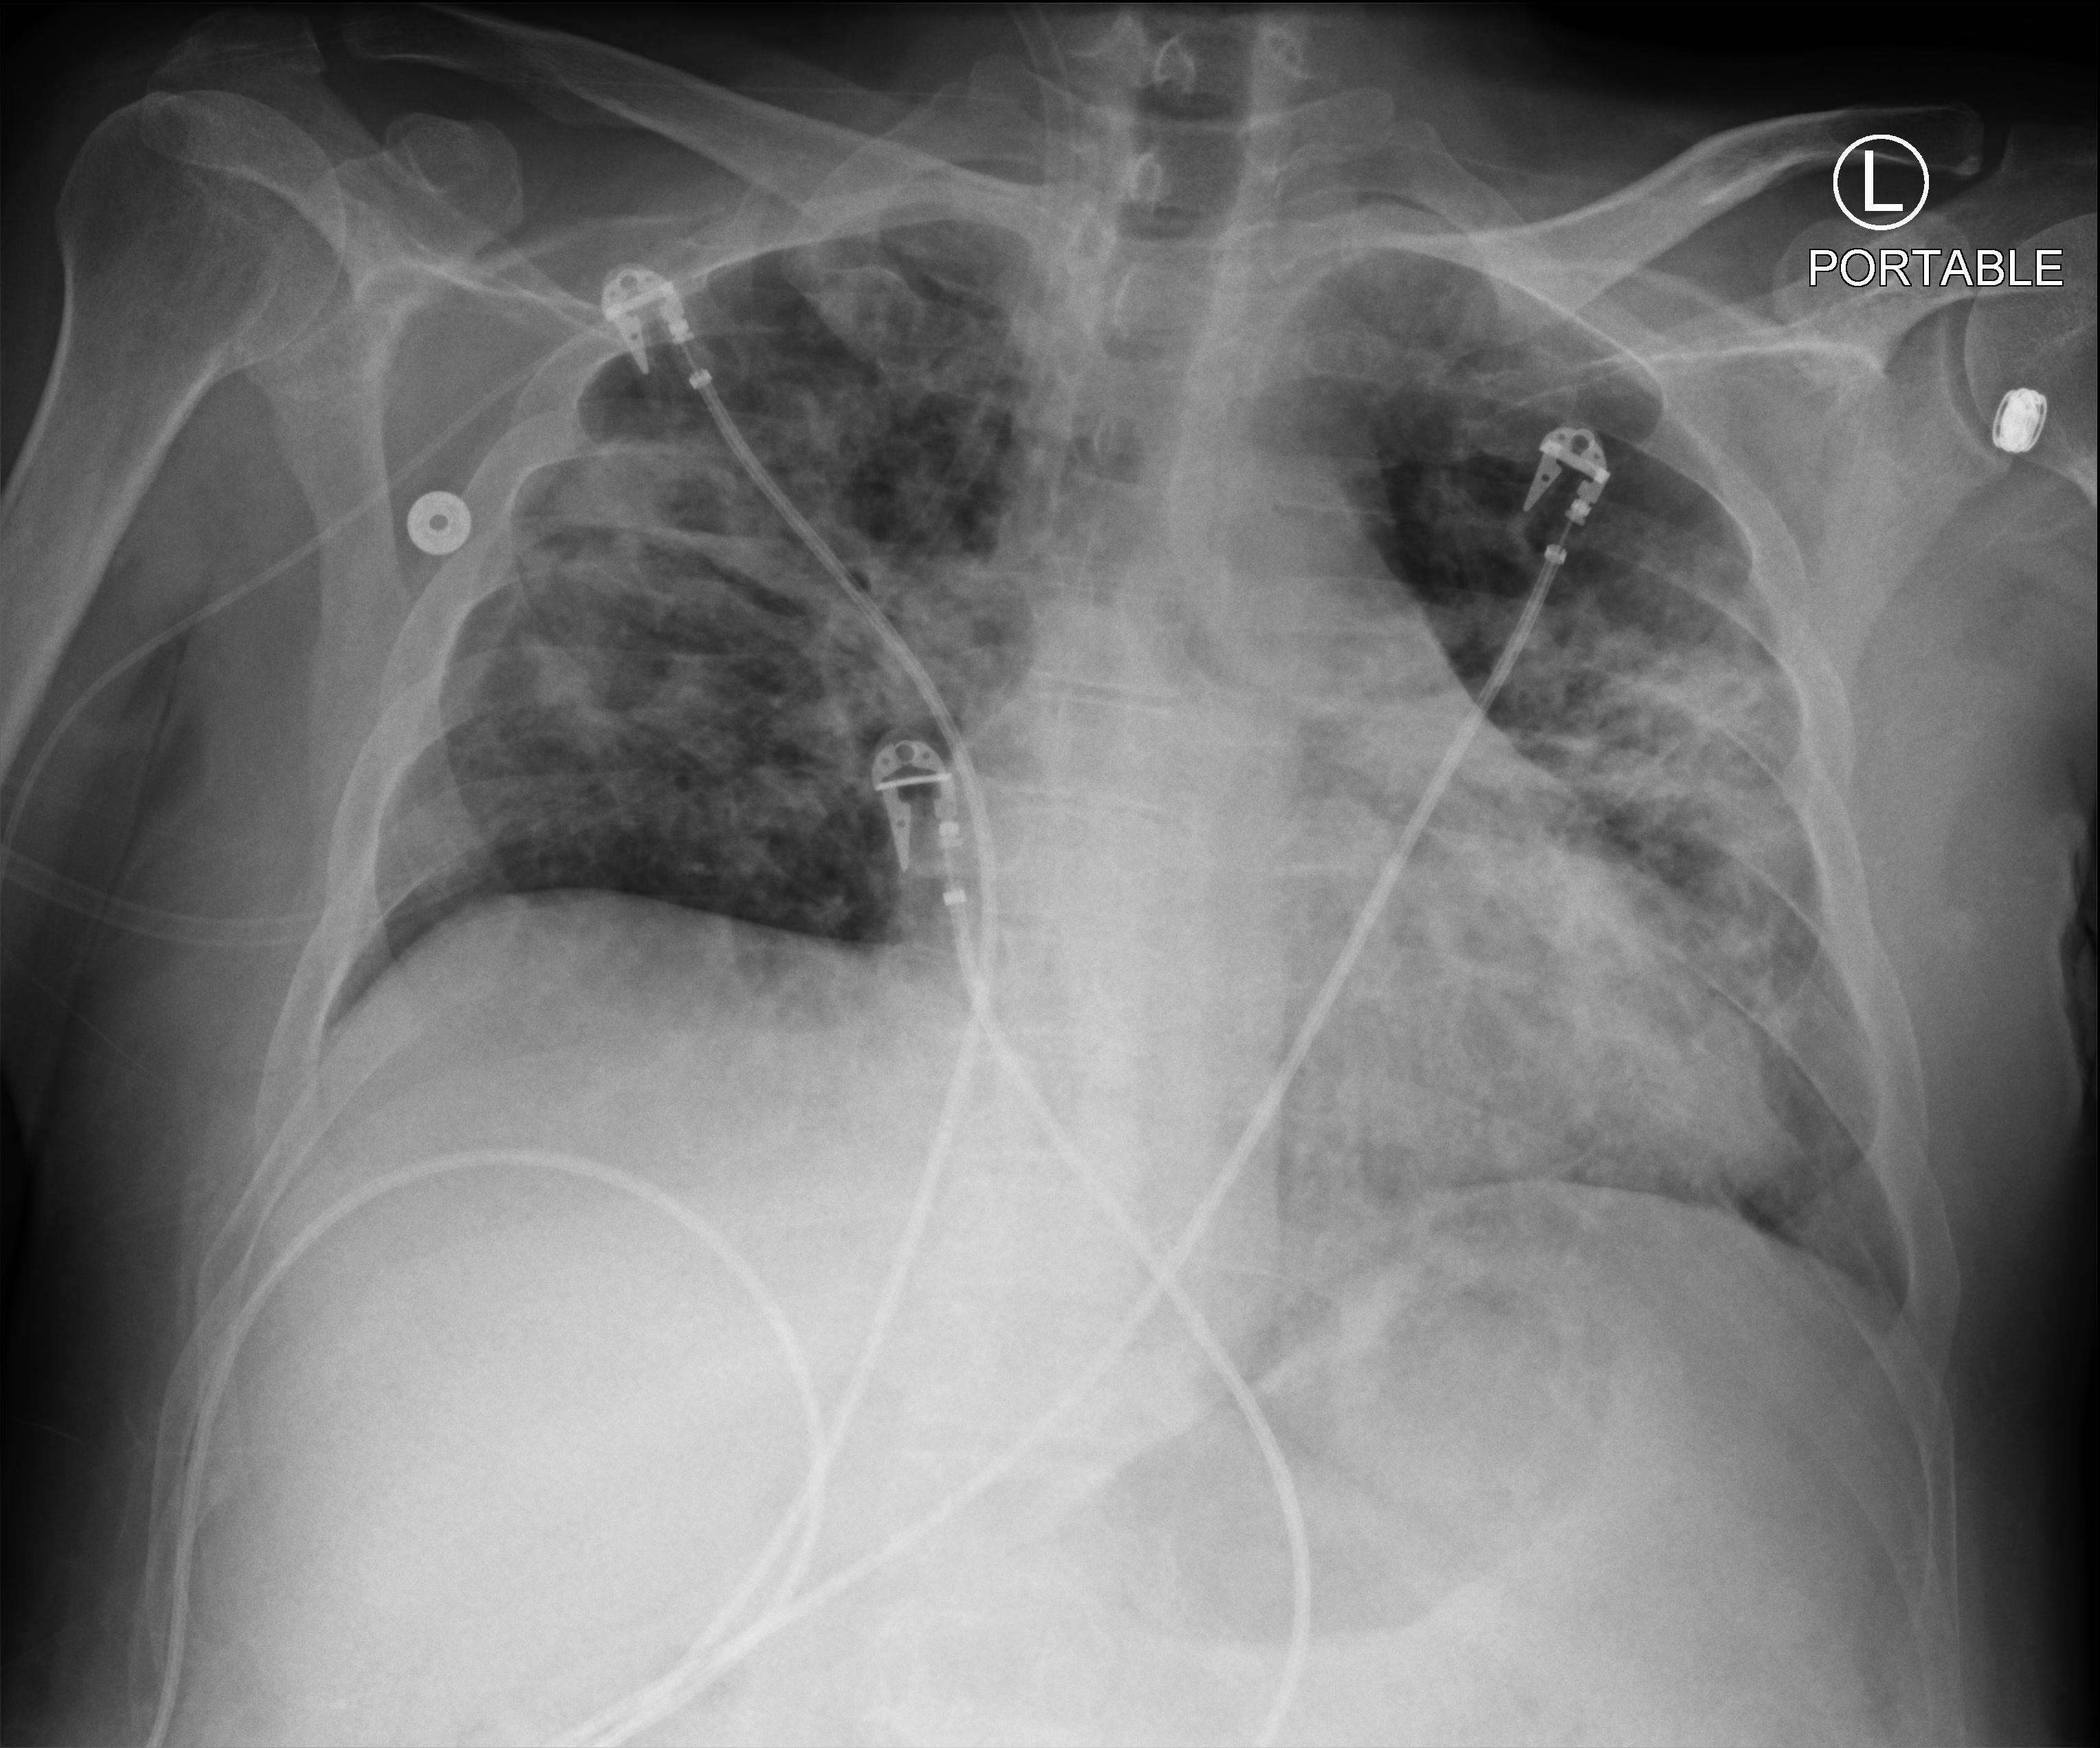
Bedside chest radiograph (computed radiography), anteroposterior (AP) projection. Male patient hospitalised with COVID-19, age 18–59 years.
From the hospital-stay record, not from the radiograph (when in the stay this image was taken is not recorded): other chronic lung disease (admission record): no; length of hospital stay: 20 days; admitted to intensive care during this hospital stay: yes.